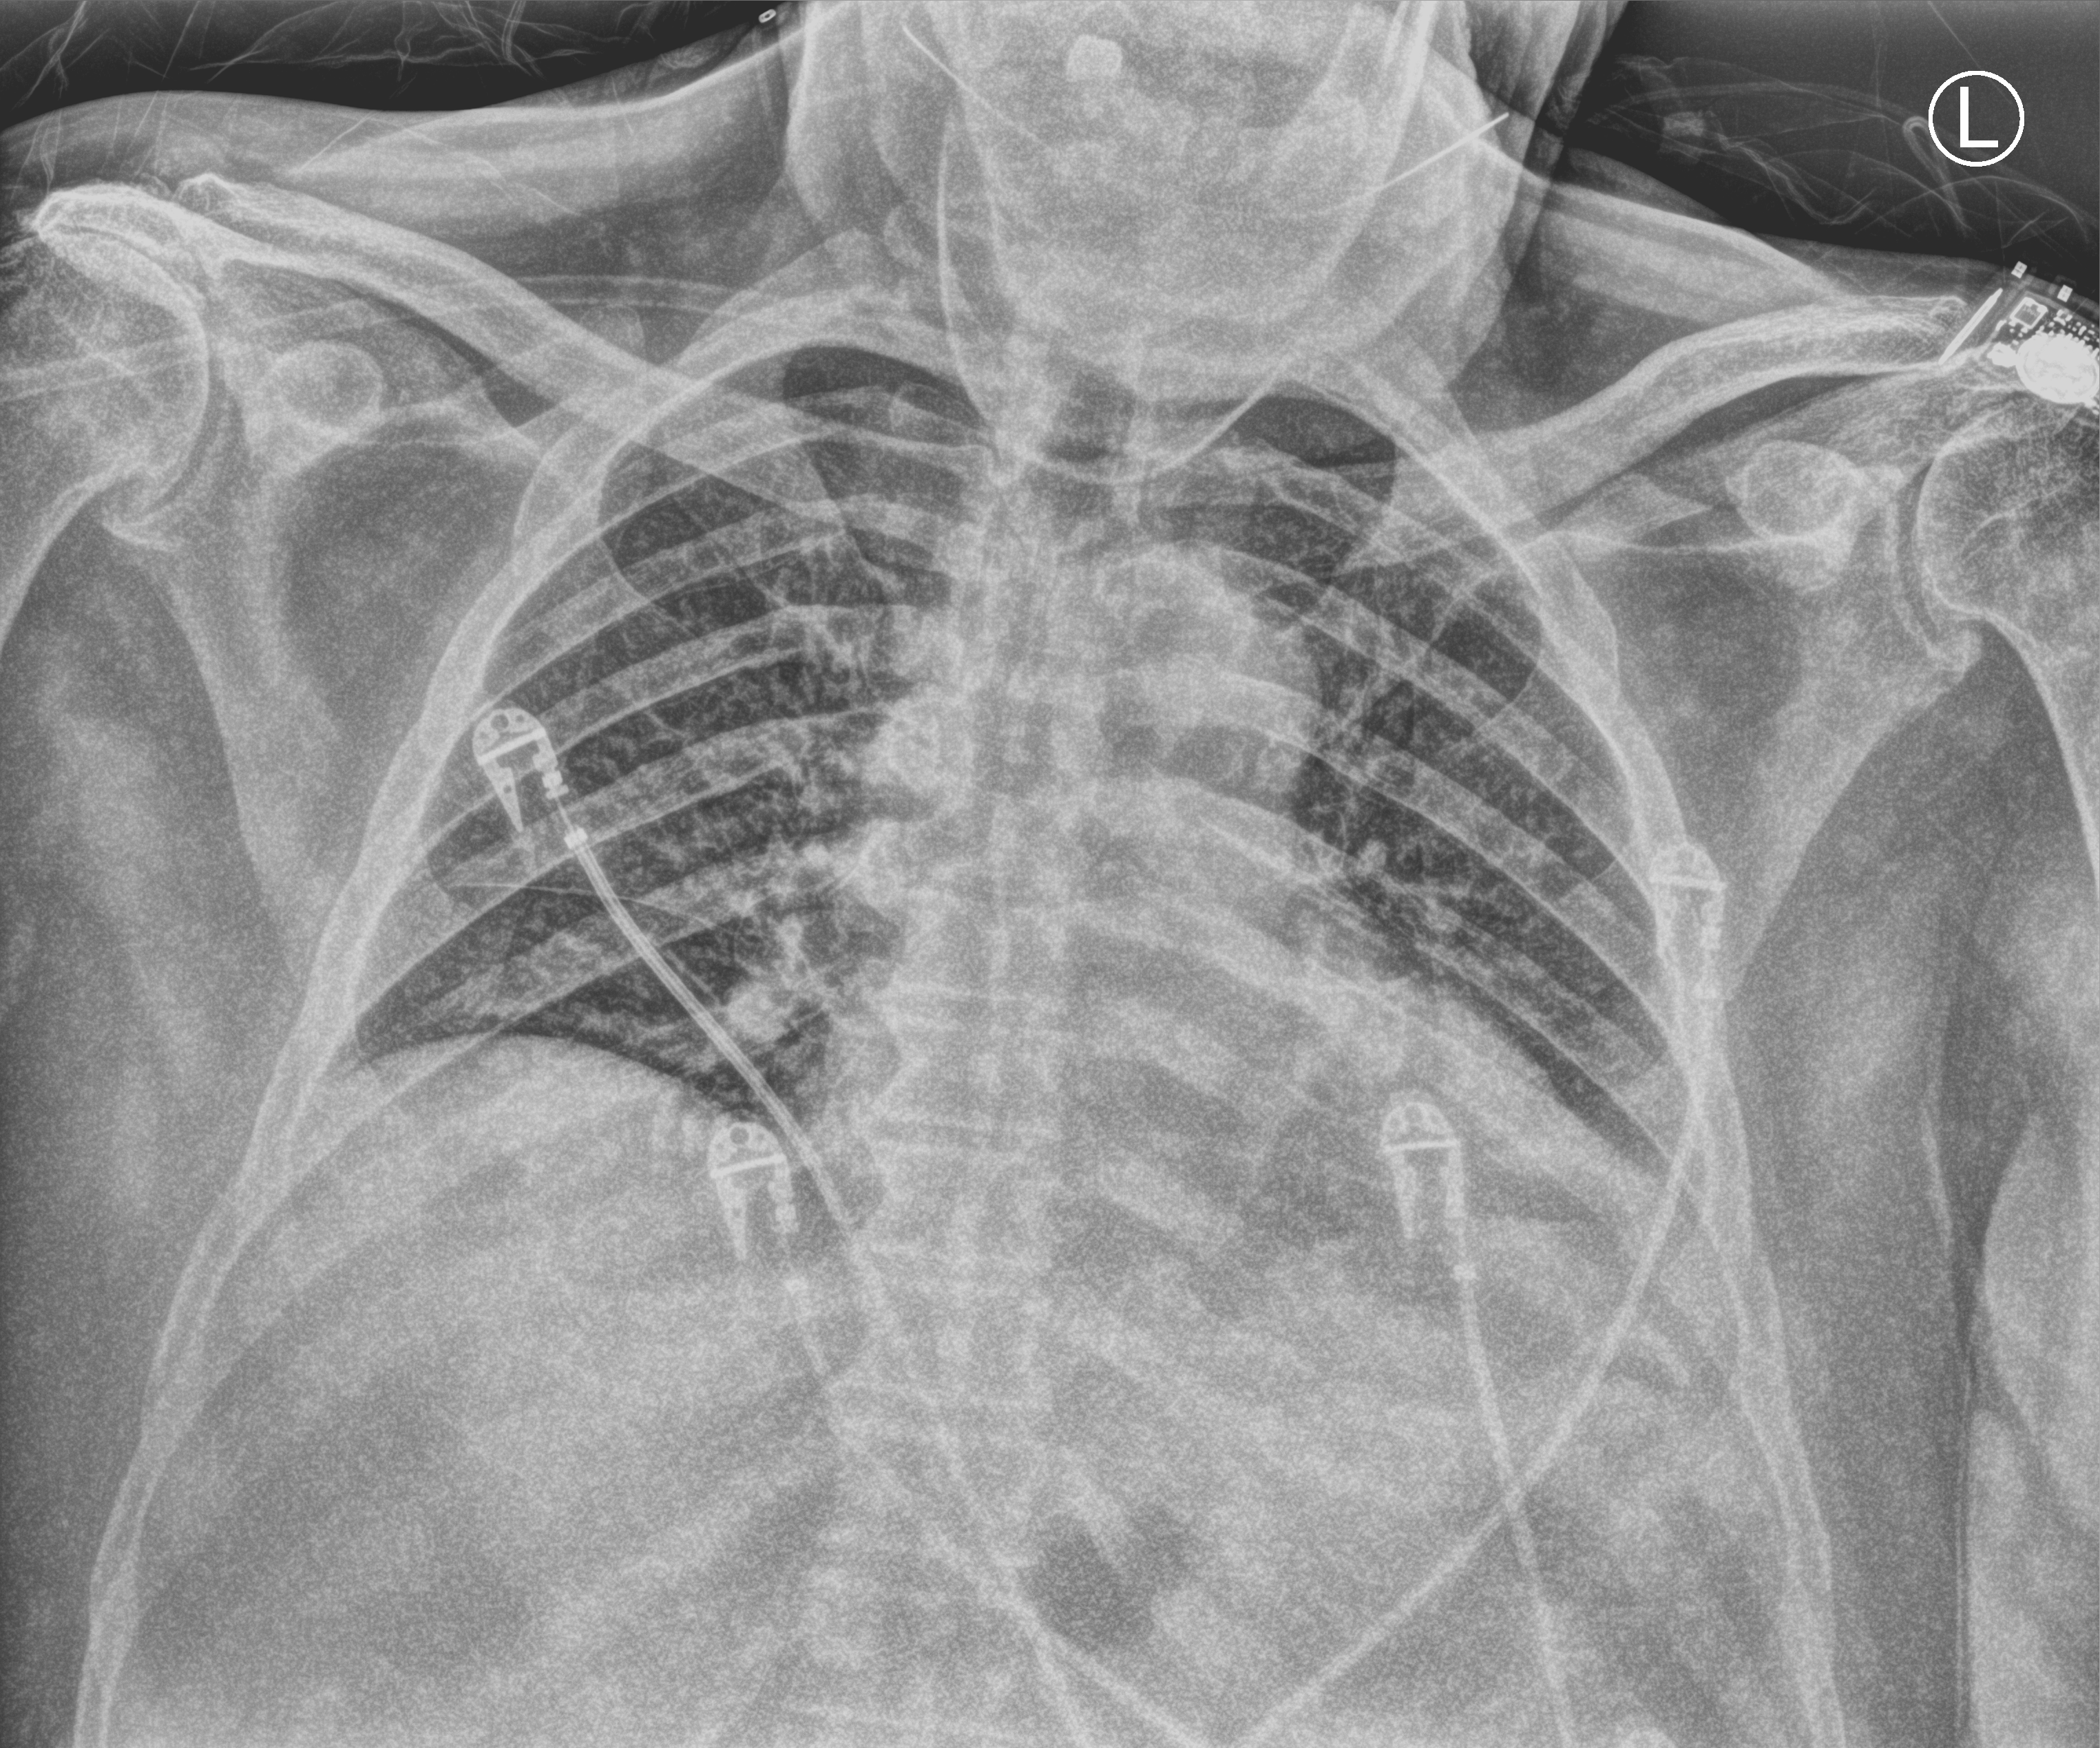
Chest X-ray (portable), anteroposterior (AP) projection. Patient hospitalised with COVID-19; male, aged 75–90 years.
Admission-level facts for this patient (not findings on this image; timing relative to this image not recorded): admitted to intensive care during this hospital stay: yes; mechanically ventilated during this hospital stay: yes; length of hospital stay: 12 days.